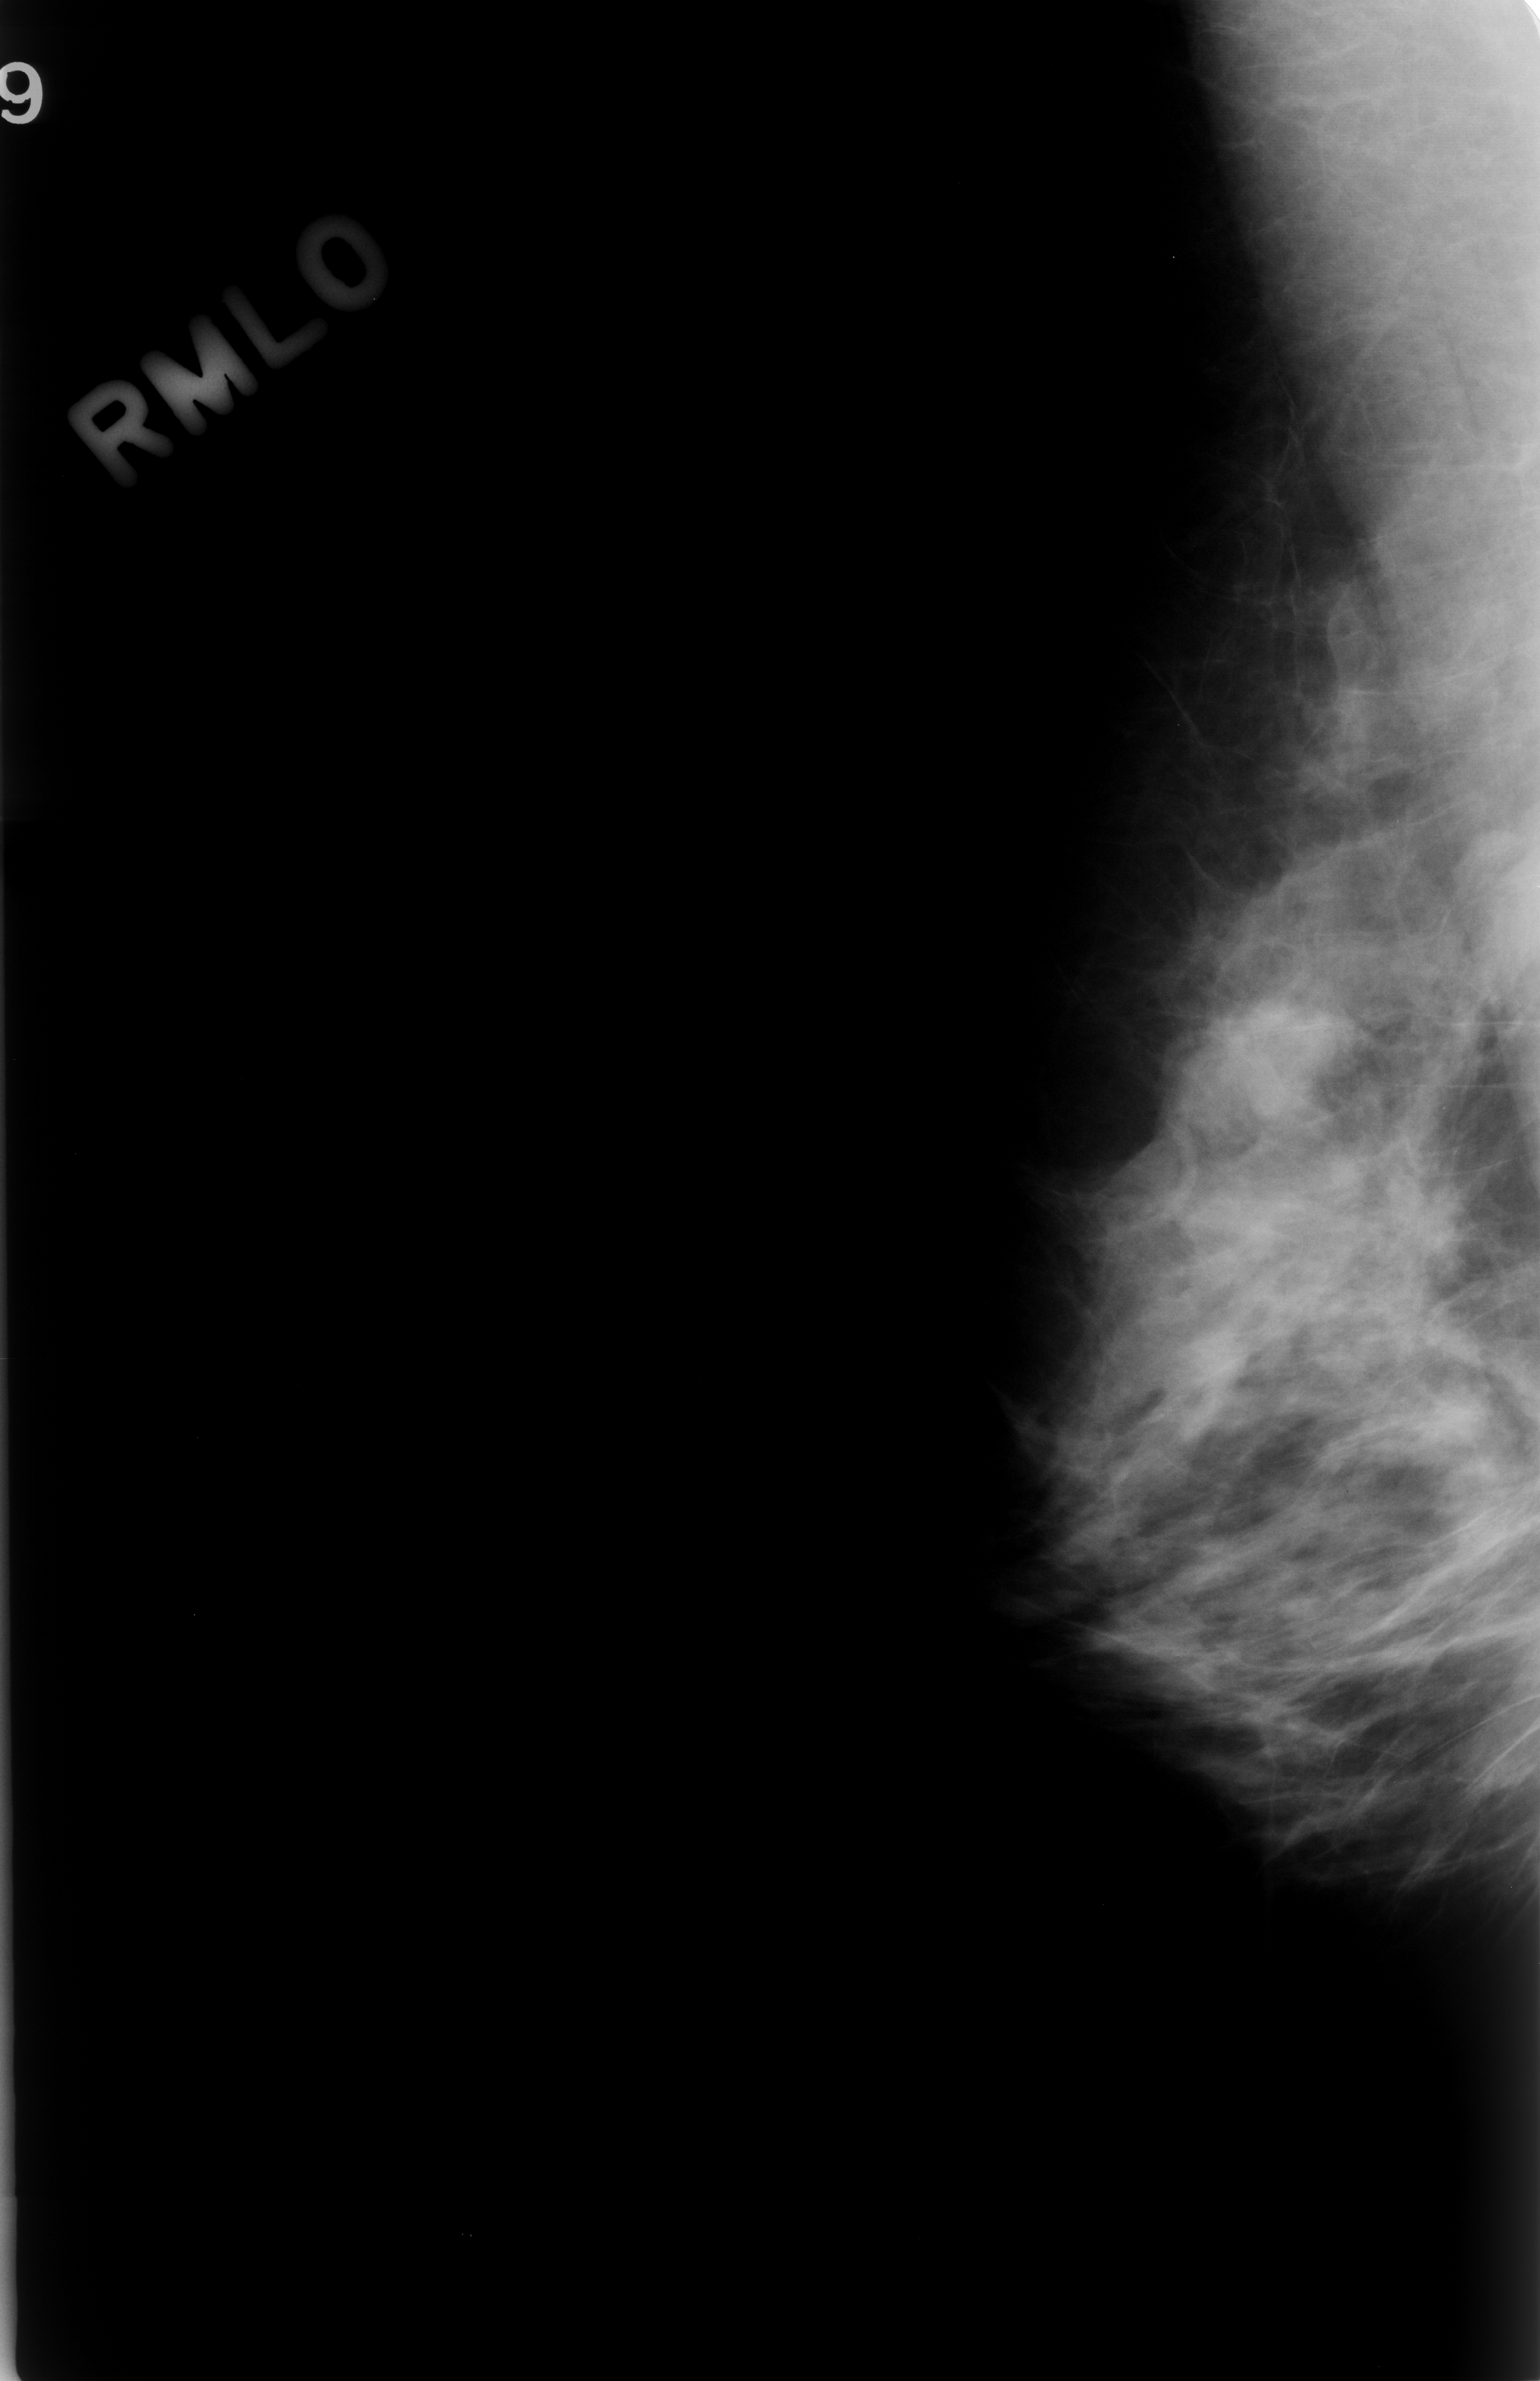
Digitized screen-film mammogram; right breast; mediolateral oblique (MLO) view; breast composition: heterogeneously dense (BI-RADS density category 3 of 4); 1540 × 2381 image matrix.
Marked abnormalities (boxes around the expert regions of interest):
- mass, shape irregular, margins spiculated; BI-RADS assessment category 4; subtlety rating 4 on a 1 (subtle) to 5 (obvious) scale; outcome (as recorded, no biopsy): benign without callback (not worked up further): bounding box [x1, y1, x2, y2] px = [1313, 1056, 1474, 1249]